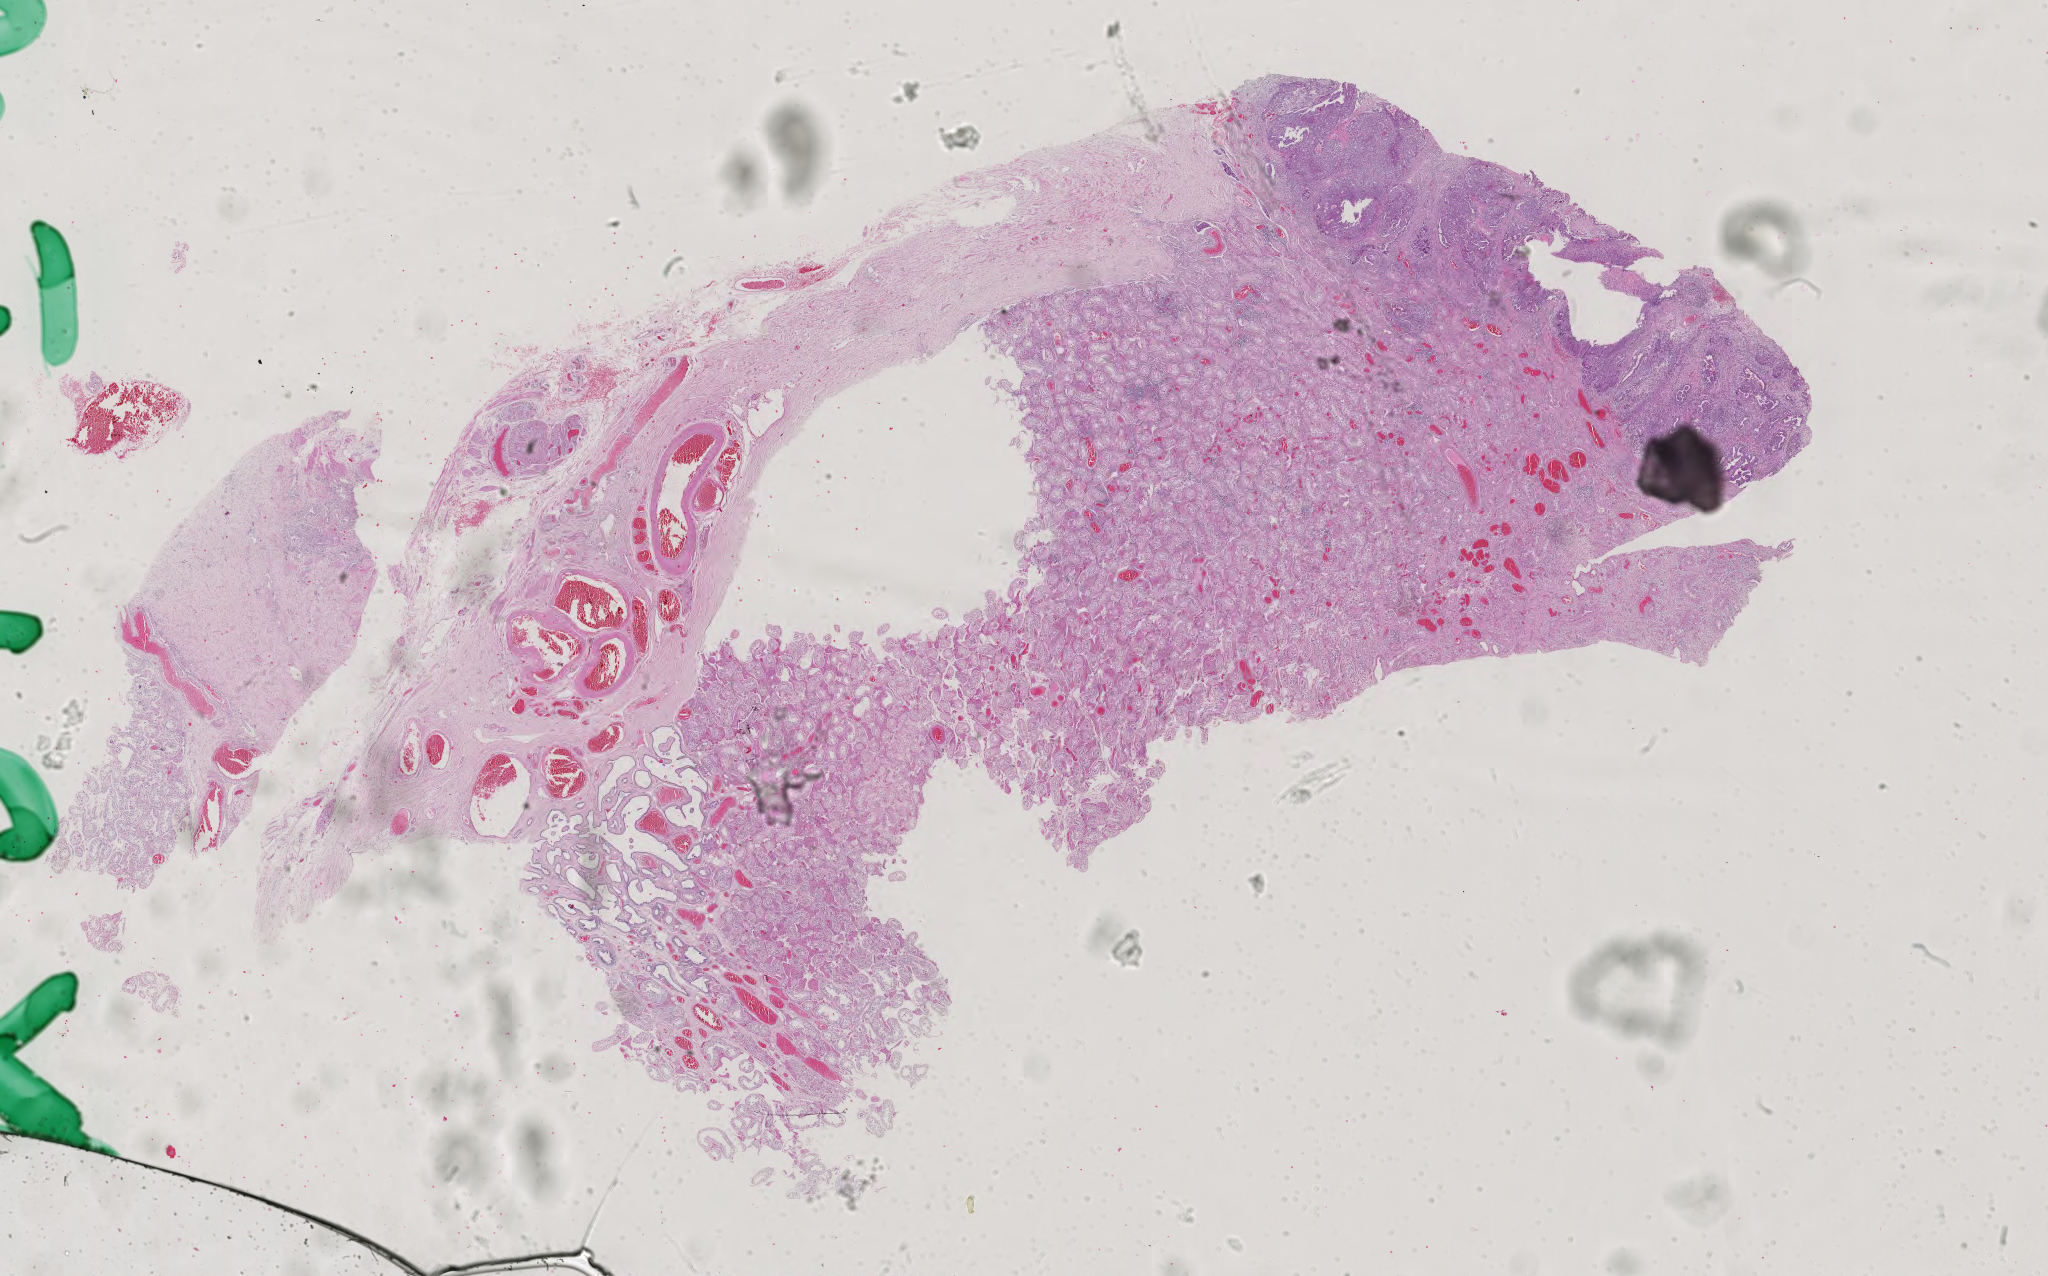
Digitized Hematoxylin and eosin (H&E) stained tissue section (whole slide) — a low-resolution overview of the entire scanned area, about 29.8 x 18.6 mm (from a 40x scan); FFPE section; testis, primary tumour sample. Patient: male, age at initial diagnosis 28 years.
Diagnosis: Mixed germ cell tumor. AJCC pathologic stage: IS (6th edition). Laterality: left.